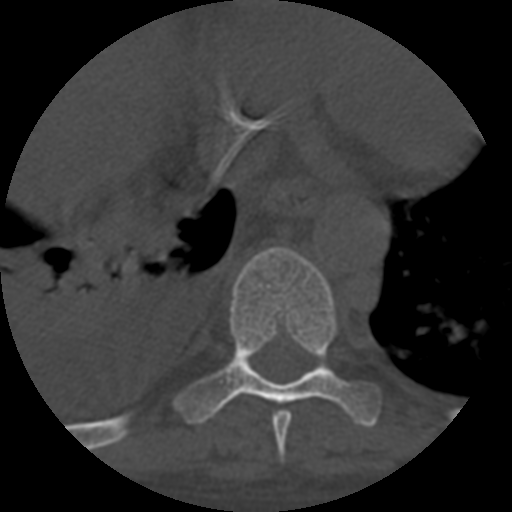
CT including the spine, one axial slice. Slice 379 of 708 in the series (ordered by position). Reconstruction kernel STANDARD. One of 3 acquisitions stored at this slice position. Bone window (W 1800 / L 400 HU). 1.25 mm slice thickness. 512 × 512 image matrix. Patient age 55 years. From the clinical record (not read from this slice): primary cancer: colon; vertebrae with lytic lesions (as recorded): T12, L1, L5.
Structures marked on this image (semi-automatically segmented with operator editing):
- T8 vertebra: bounding box <272,410,292,461> (left, top, right, bottom; pixels)
- T9 vertebra: <171,247,381,427>